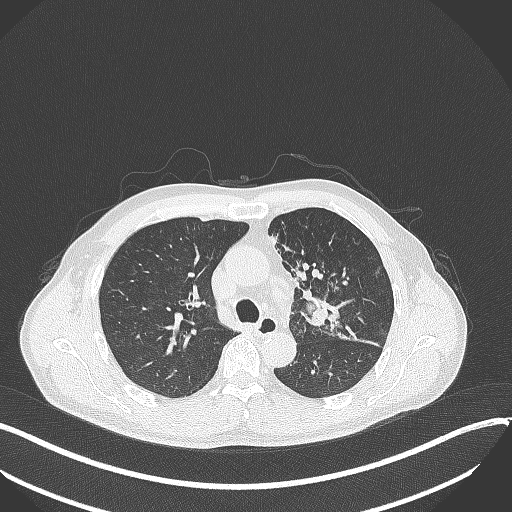
Chest CT, one axial slice. Slice 232 of 411 in the series (ordered by position). Reconstruction kernel B70f. 120 kVp. Lung window (W 1500 / L -600 HU). 1 mm slice thickness. 512 × 512 image matrix, field of view 400 × 400 mm. Male patient, age 56 years. From the clinical record (not read from this slice): clinical TNM (as recorded): T2a N0 M0.
Annotated regions visible in this slice (bounding box drawn by a radiologist):
- lung tumour (recorded histology: squamous cell carcinoma): box from (x=299, y=285) to (x=350, y=330) px